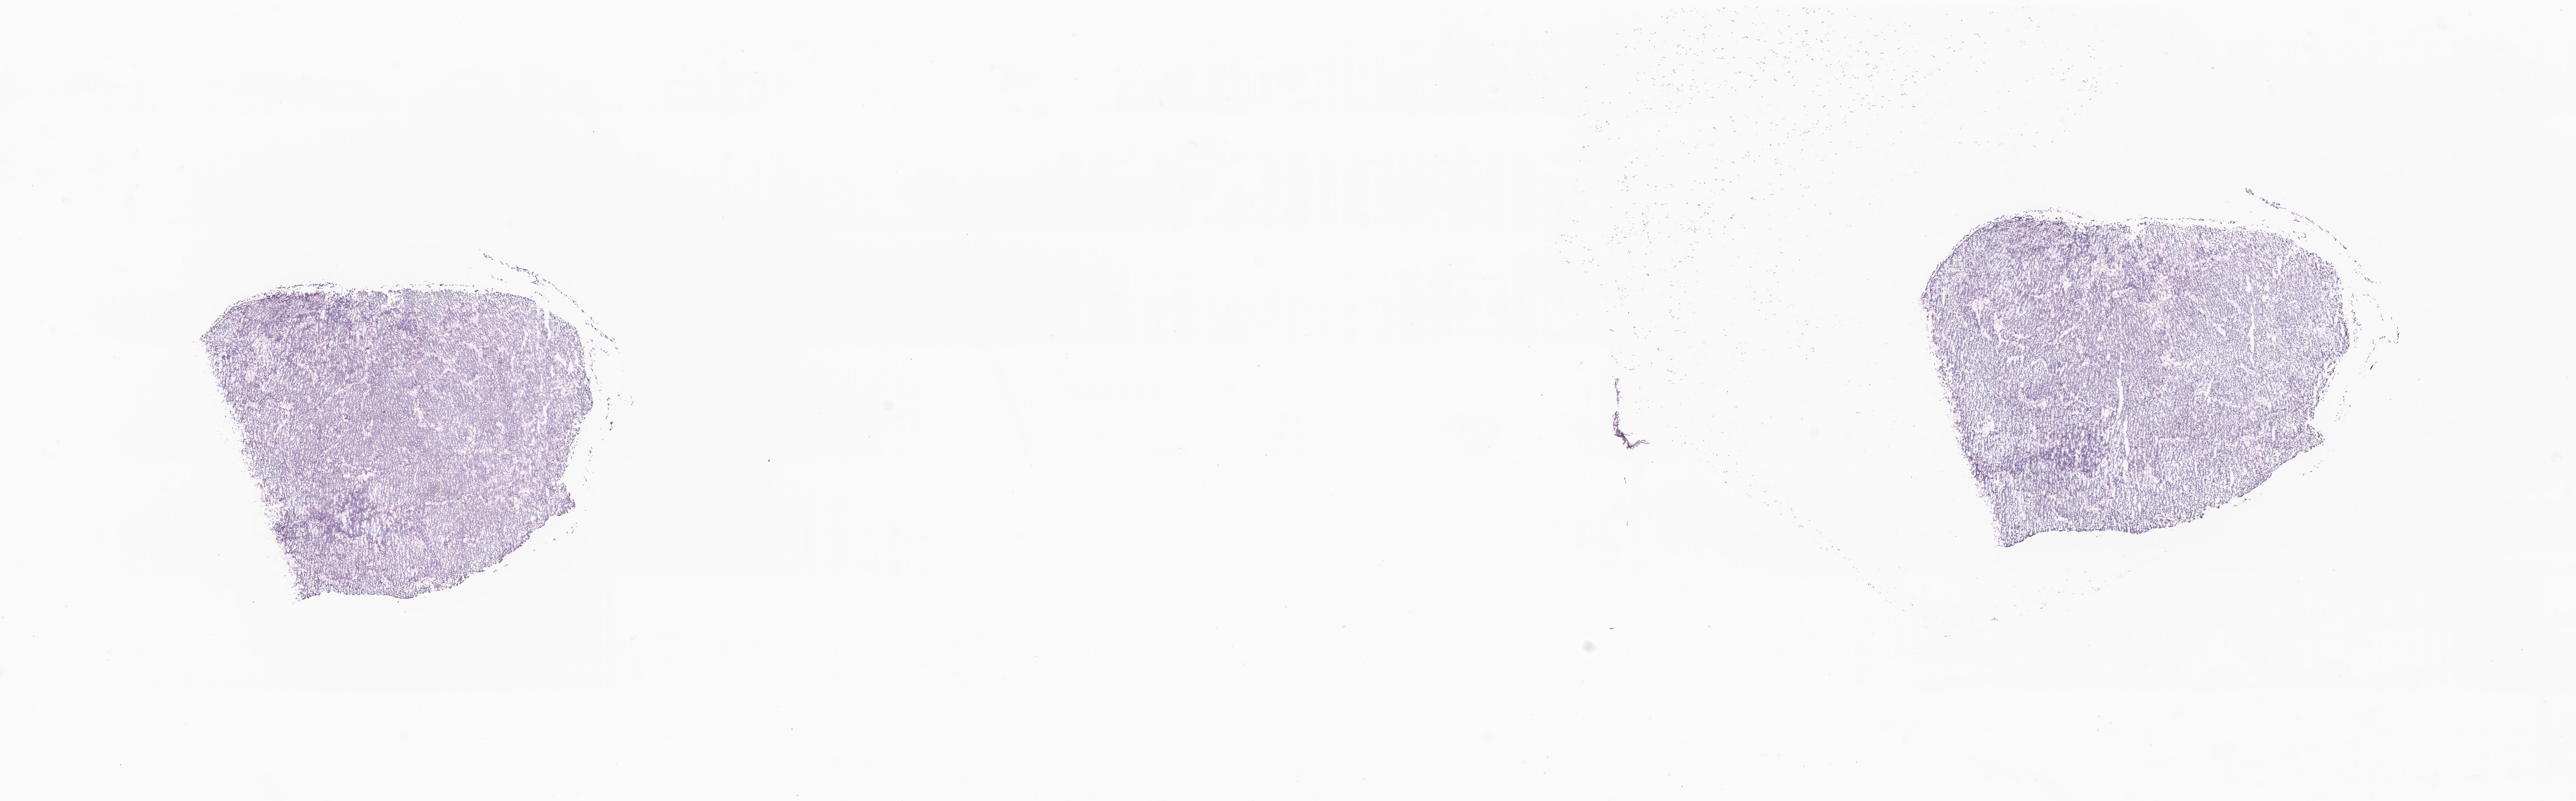
Whole-slide image, H&E stain of tumor tissue from the cerebellum — shown as a low-resolution overview of the whole scanned area (about 23.9 x 7.4 mm); frozen section (OCT-embedded). Male patient, age 105 months (8 years 9 months).
- diagnosis: Medulloblastoma, NOS